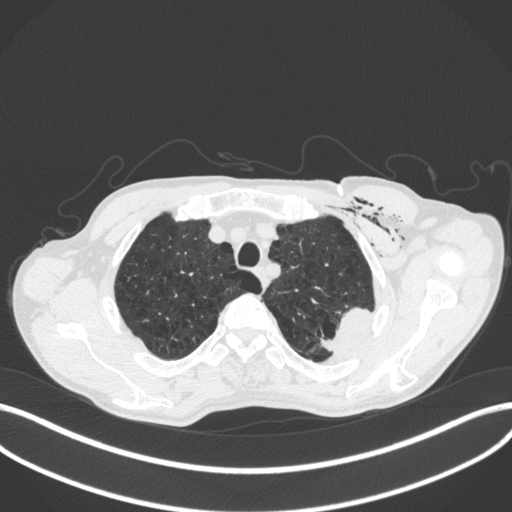
Chest CT, one axial slice. Slice 348 of 416 in the series (ordered by position). Reconstruction kernel B31f. 120 kVp. Lung window (W 1500 / L -600 HU). 1 mm slice thickness. 512 × 512 image matrix, field of view 400 × 400 mm. Patient: male, 58 years. From the clinical record (not read from this slice): clinical TNM (as recorded): T3 N0 M0.
Annotated regions visible in this slice (bounding box drawn by a radiologist):
- lung tumour (recorded histology: adenocarcinoma): bounding box <315,303,378,357> (left, top, right, bottom; pixels)